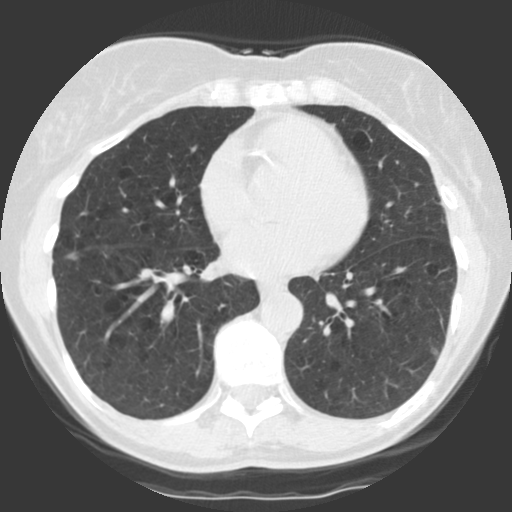
Low-dose screening chest CT, one axial slice. Slice 52 of 123 in the series (ordered by position). 140 kVp. Lung window (W 1500 / L -600 HU). 512 × 512 image matrix, field of view 290 × 290 mm.
Structures marked on this image (manually delineated by an expert):
- lesion 1 (tumor, middle lobe of right lung): bounding box [x1, y1, x2, y2] px = [69, 254, 74, 259]